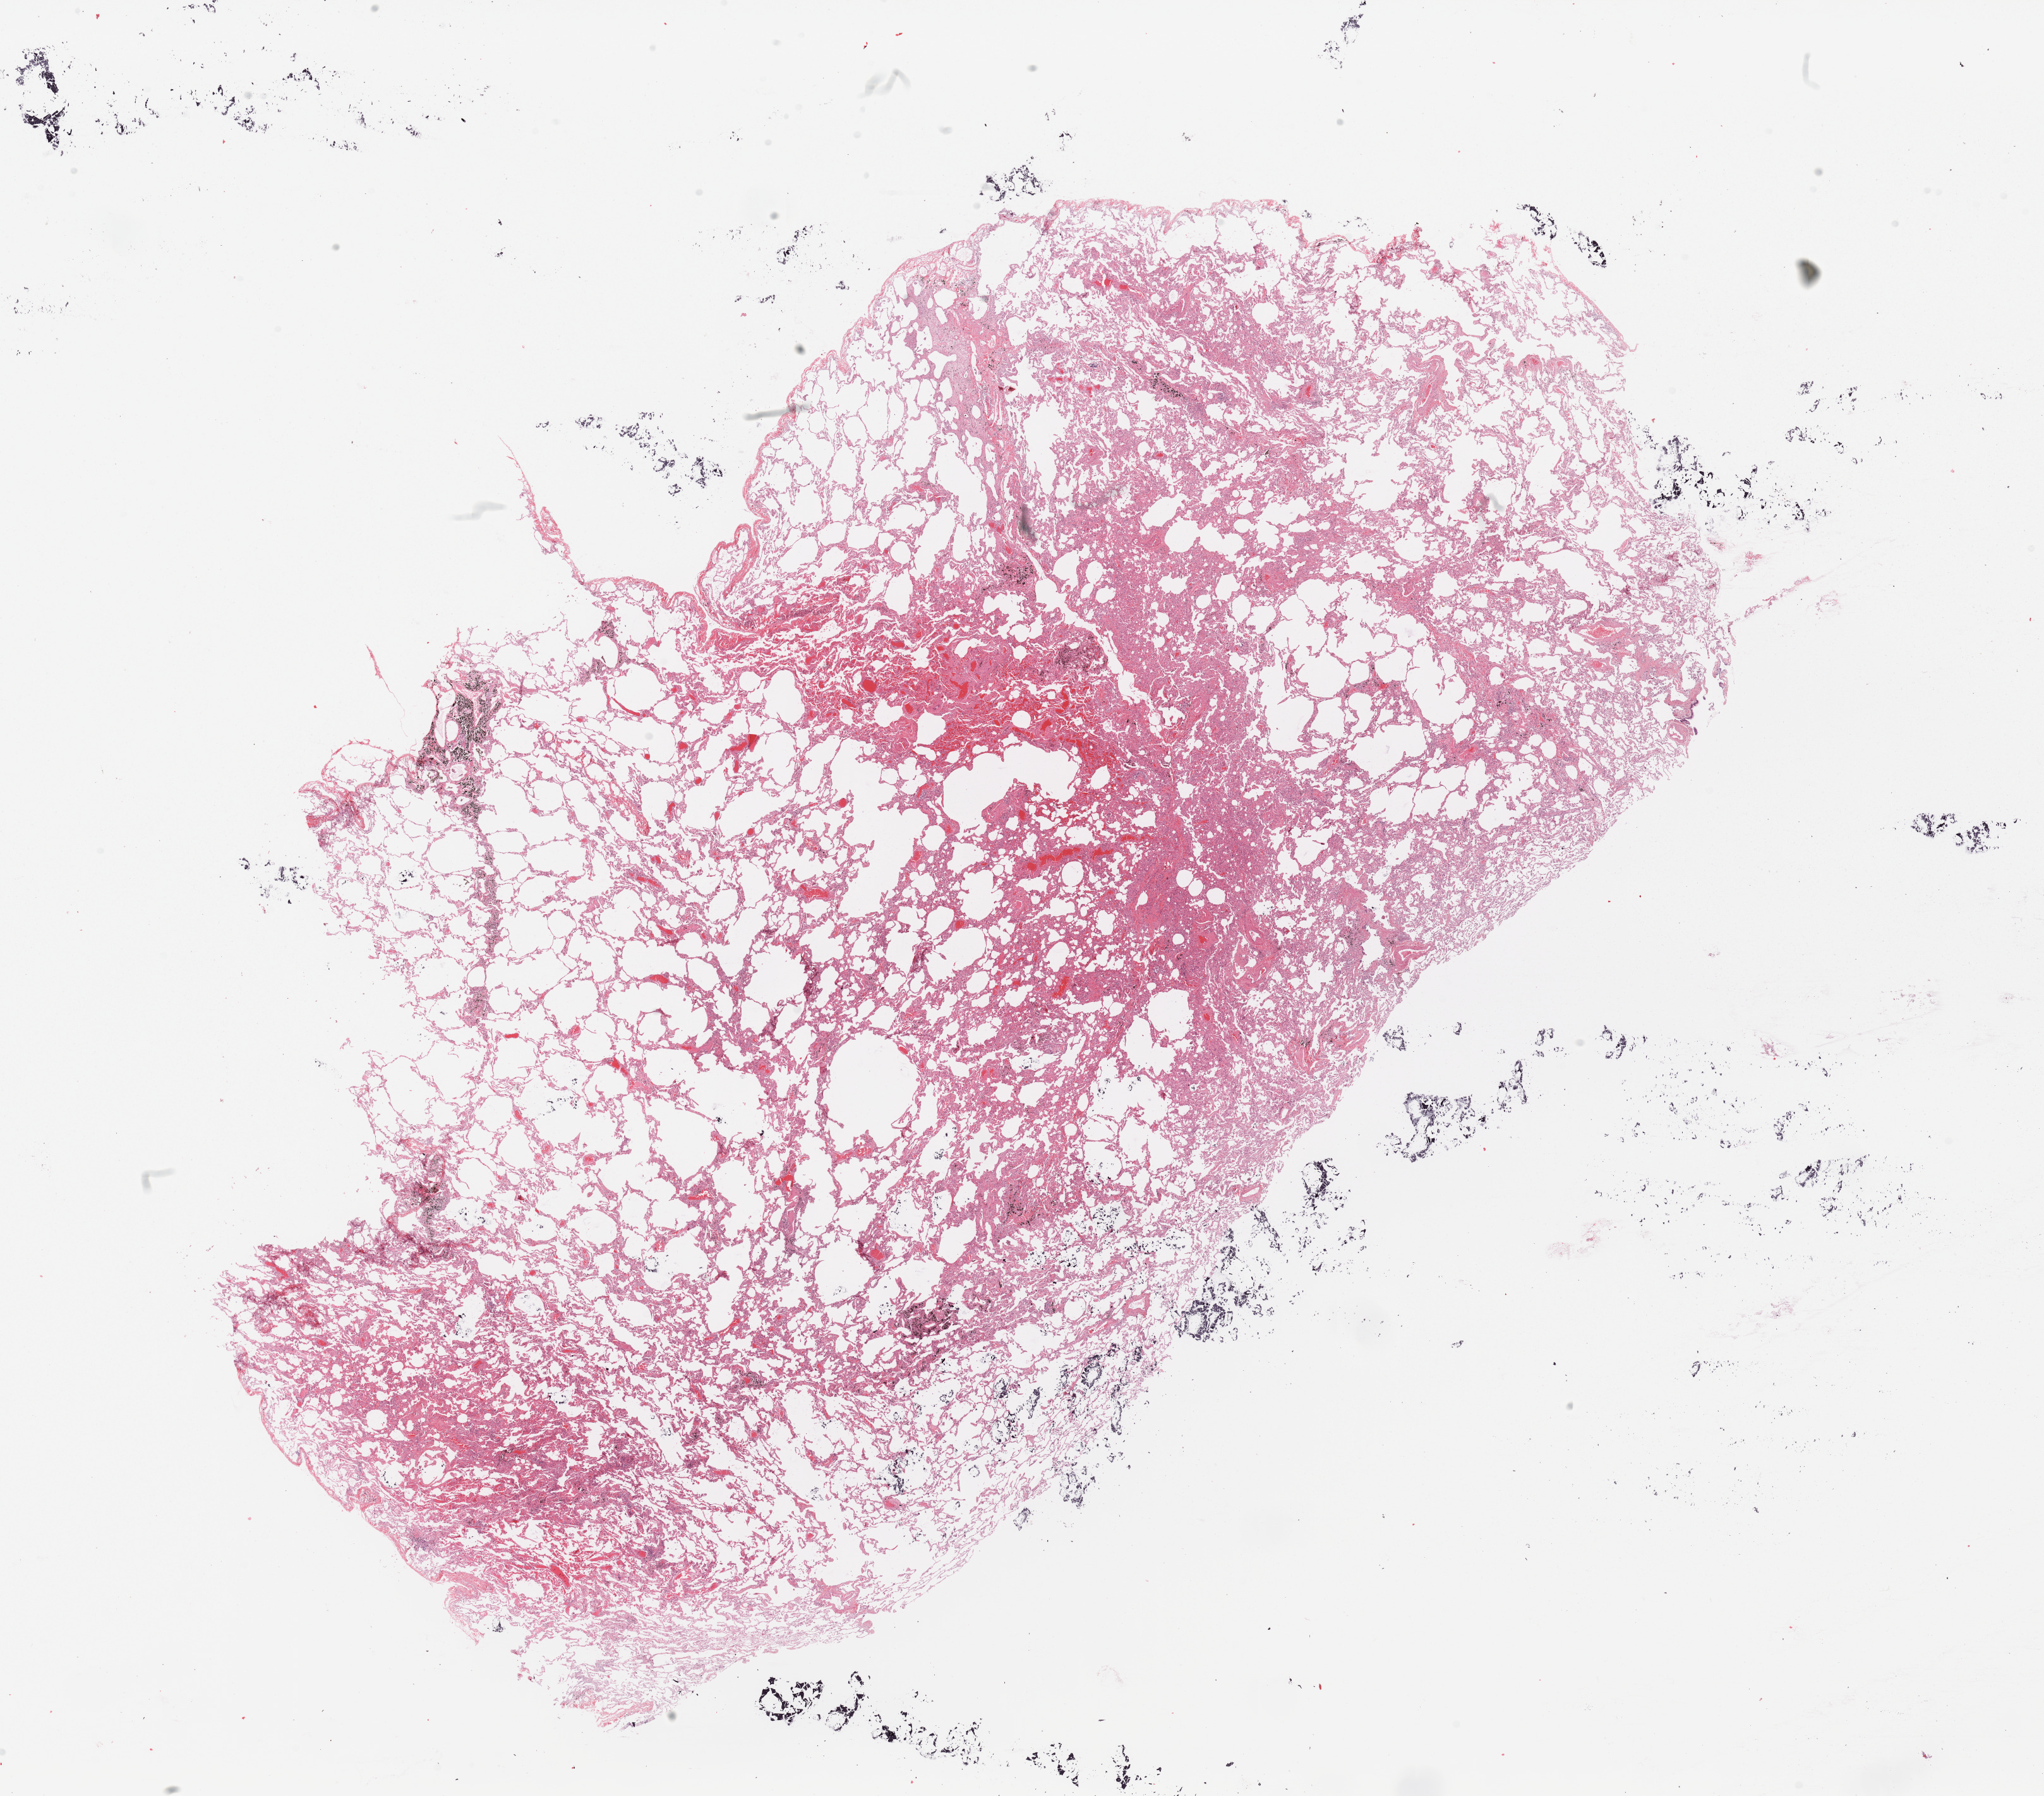
Hematoxylin and eosin (H&E) stained whole-slide image — a low-resolution overview of the entire scanned area, about 25.6 x 22.5 mm (acquisition: 20x scan); normal (non-tumour) tissue sample, sampled site: lung. Patient: male, age 61 years.
This section: normal (non-tumour) tissue from the same patient. Patient diagnosis: Squamous cell carcinoma, NOS.